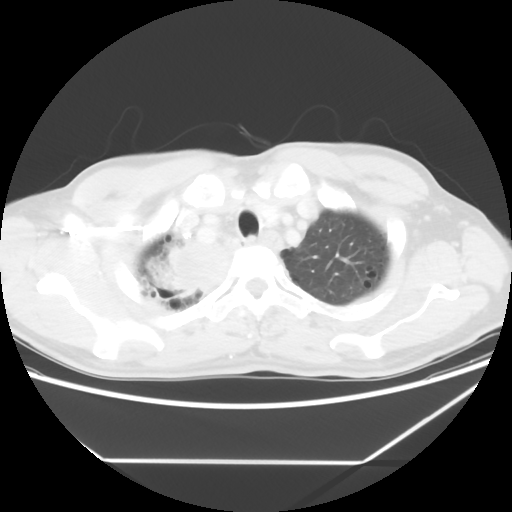
Chest CT, one axial slice. Position 53 of 60 along the scan axis. Reconstruction kernel STANDARD. 120 kVp. Lung window (W 1500 / L -600 HU). 512 × 512 image matrix. Patient: male, 58 years. Case-level facts recorded for this patient, not image findings: clinical TNM (as recorded): T2 N2 M0.
Outlined on this slice (rectangle marked by the reading radiologist):
- lung tumour (recorded histology: squamous cell carcinoma): bounding box <163,236,234,302> (left, top, right, bottom; pixels)